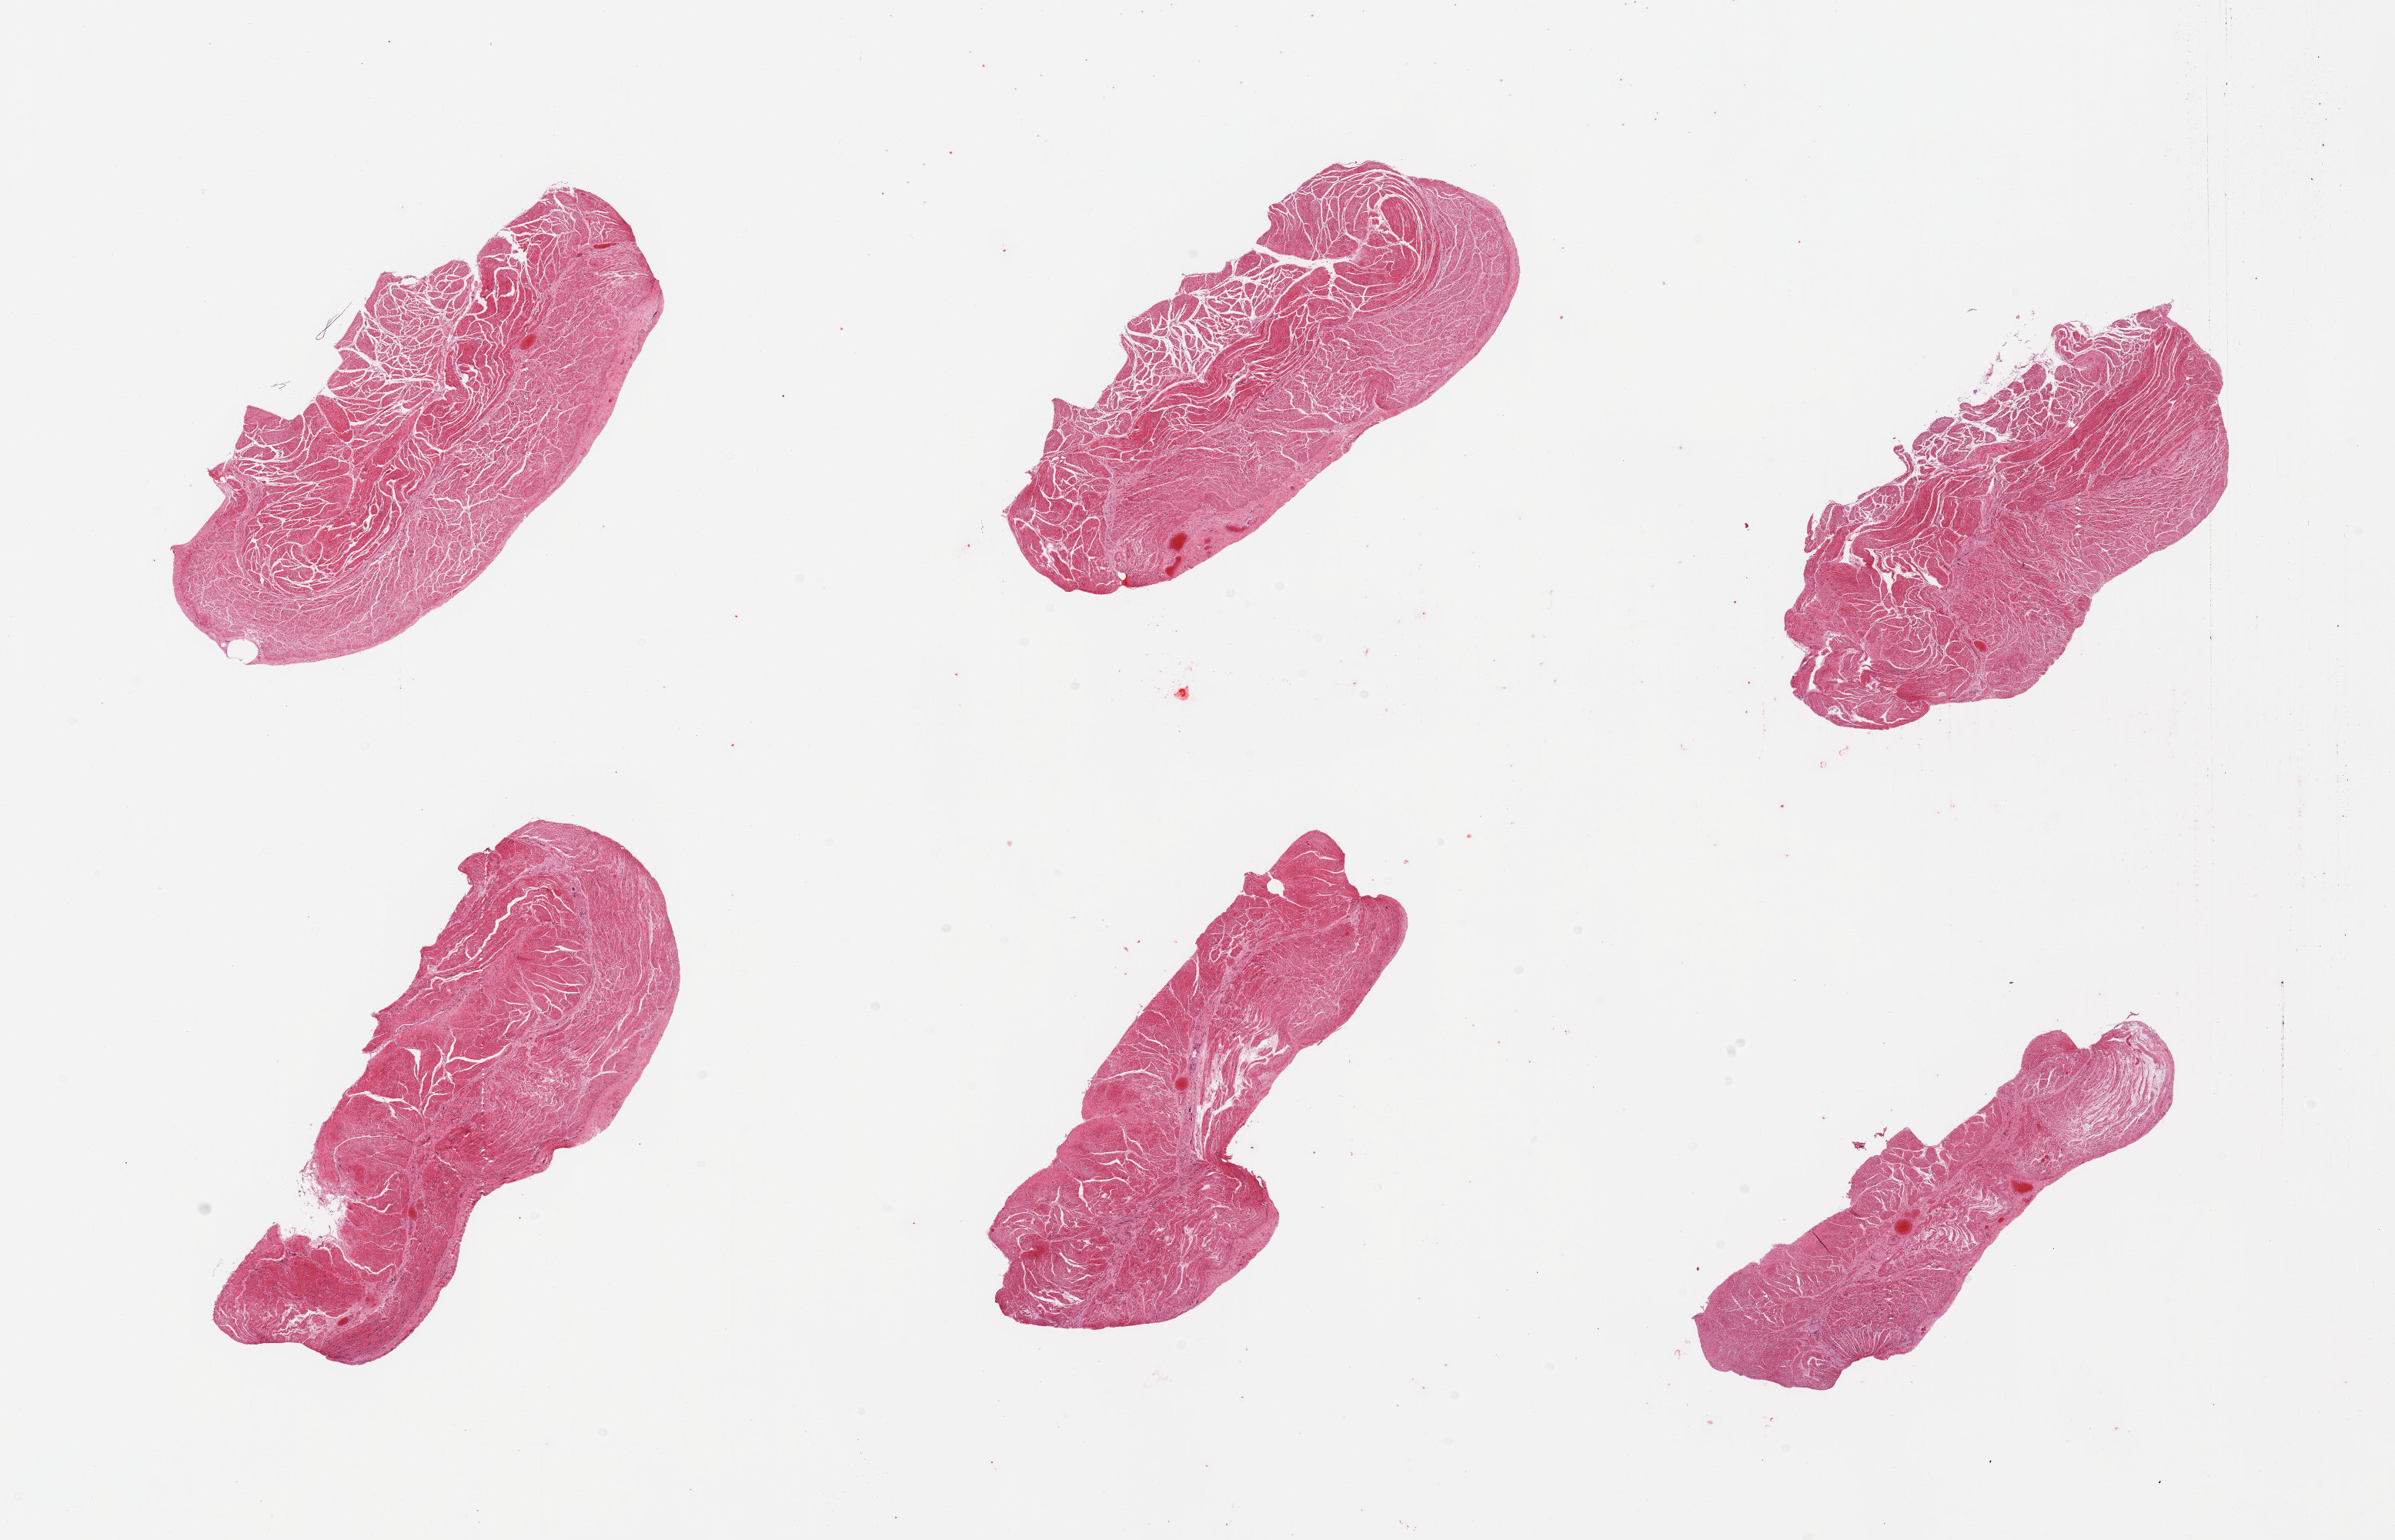
H&E whole-slide image, brightfield — low-resolution overview of the scanned area, about 24.6 x 15.8 mm (from a 20x scan), PAXgene-fixed paraffin-embedded (PFPE) section, sampled site (target tissue): esophageal muscle, tissue donor sample. Donor sex: female.
* pathologist's review note for this sample: 6 pieces; well trimmed